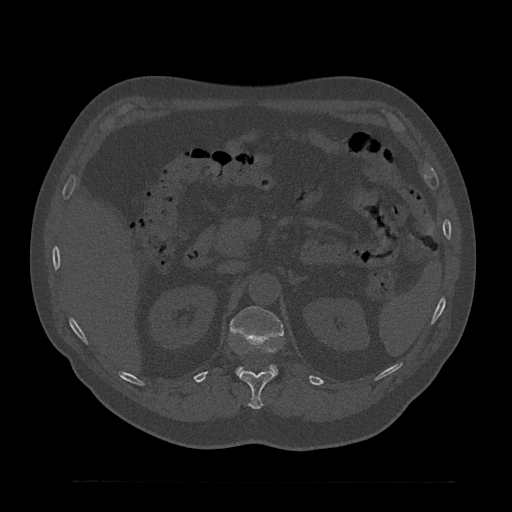
CT including the spine, one axial slice; position 202 of 797 along the scan axis; reconstruction kernel Br40s/3; bone window (W 1800 / L 400 HU); 0.5 mm slice thickness; 512 × 512 image matrix. Patient: male, 61 years. From the clinical record (not read from this slice): primary cancer: prostate.
Outlined on this slice (semi-automatically segmented with operator editing):
- L1 vertebra: bounding box [x1, y1, x2, y2] px = [230, 306, 283, 375]
- T12 vertebra: [239, 371, 274, 410]